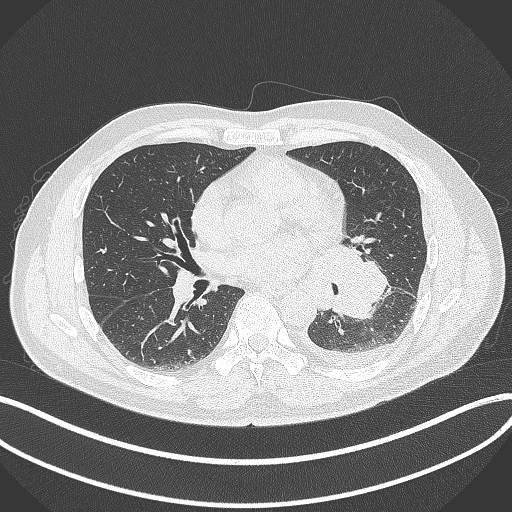
Chest CT, one axial slice. Position 176 of 342 along the scan axis. Reconstruction kernel B70f. 120 kVp. Lung window (W 1500 / L -600 HU). 1 mm slice thickness. 512 × 512 image matrix, field of view 400 × 400 mm. Patient: male, 58 years. From the clinical record (not read from this slice): clinical TNM (as recorded): T3 N1 M1b.
Outlined on this slice (rectangle marked by the reading radiologist):
- lung tumour (recorded histology: small cell carcinoma): bounding box <315,237,393,322> (left, top, right, bottom; pixels)